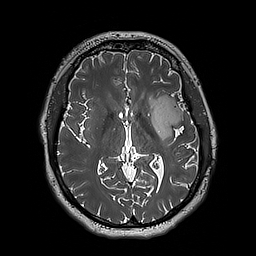
Brain MRI from a brain-tumour surgery series, one axial slice. Position 103 of 192 along the scan axis. 1 mm slice thickness. 256 × 256 image matrix, field of view 250 × 250 mm. From the clinical record (not read from this slice): histopathology: Astrocytoma; WHO grade: 3; IDH mutation: yes; tumour location: Left Insular.
Outlined on this slice (expert manual segmentation):
- tumour: box from (x=147, y=94) to (x=183, y=140) px